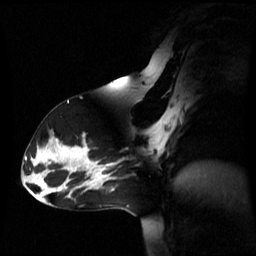
Breast MRI (dynamic contrast-enhanced), one sagittal slice; position 35 of 60 along the scan axis; dynamic contrast-enhanced series, image 2 of 3 at this slice position (ordered by acquisition); 1.5 T; TE 4.2 ms, TR 8.4 ms; 256 × 256 image matrix, field of view 270 × 270 mm. Female patient, age 39 years. Case-level facts recorded for this patient, not image findings: setting: breast cancer imaged before/during neoadjuvant chemotherapy; receptor status: triple-negative.
Annotated regions visible in this slice (semi-automatically segmented with operator editing):
- analysis volume of interest (the breast-tissue region the enhancement analysis was run in; not a lesion): bounding box [x1, y1, x2, y2] px = [105, 149, 148, 179]
- tumour enhancement mask (voxels above the 70 % enhancement threshold inside the analysis volume of interest): [105, 162, 118, 179]